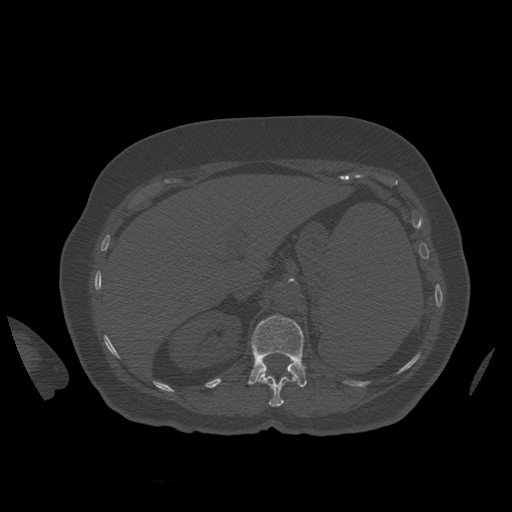
CT including the spine, one axial slice; reconstruction kernel STANDARD; bone window (W 1800 / L 400 HU); 512 × 512 image matrix, field of view 404 × 404 mm. Patient age 81 years. Case-level facts recorded for this patient, not image findings: primary cancer: renal; vertebrae with lytic lesions (as recorded): L1.
Annotated regions visible in this slice (semi-automatic segmentation, software-assisted and operator-edited):
- L1 vertebra: bounding box (x1, y1, x2, y2) in pixels: (248, 315, 307, 388)
- T12 vertebra: (258, 372, 297, 407)